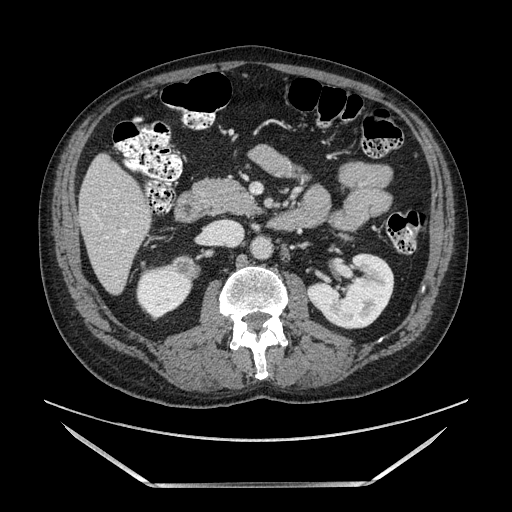
Contrast-enhanced abdominal CT, one axial slice; position 49 of 185 along the scan axis; soft-tissue window (W 400 / L 40 HU); 512 × 512 image matrix, field of view 440 × 440 mm. Male patient. Case-level facts recorded for this patient, not image findings: diagnosis: adrenocortical carcinoma; tumour side: right adrenal; tumour size at pathology: 10.3 cm; Ki-67 index: 20 %.
Structures marked on this image (semi-automatically segmented with operator editing):
- mass: bounding box [x1, y1, x2, y2] px = [174, 254, 198, 278]